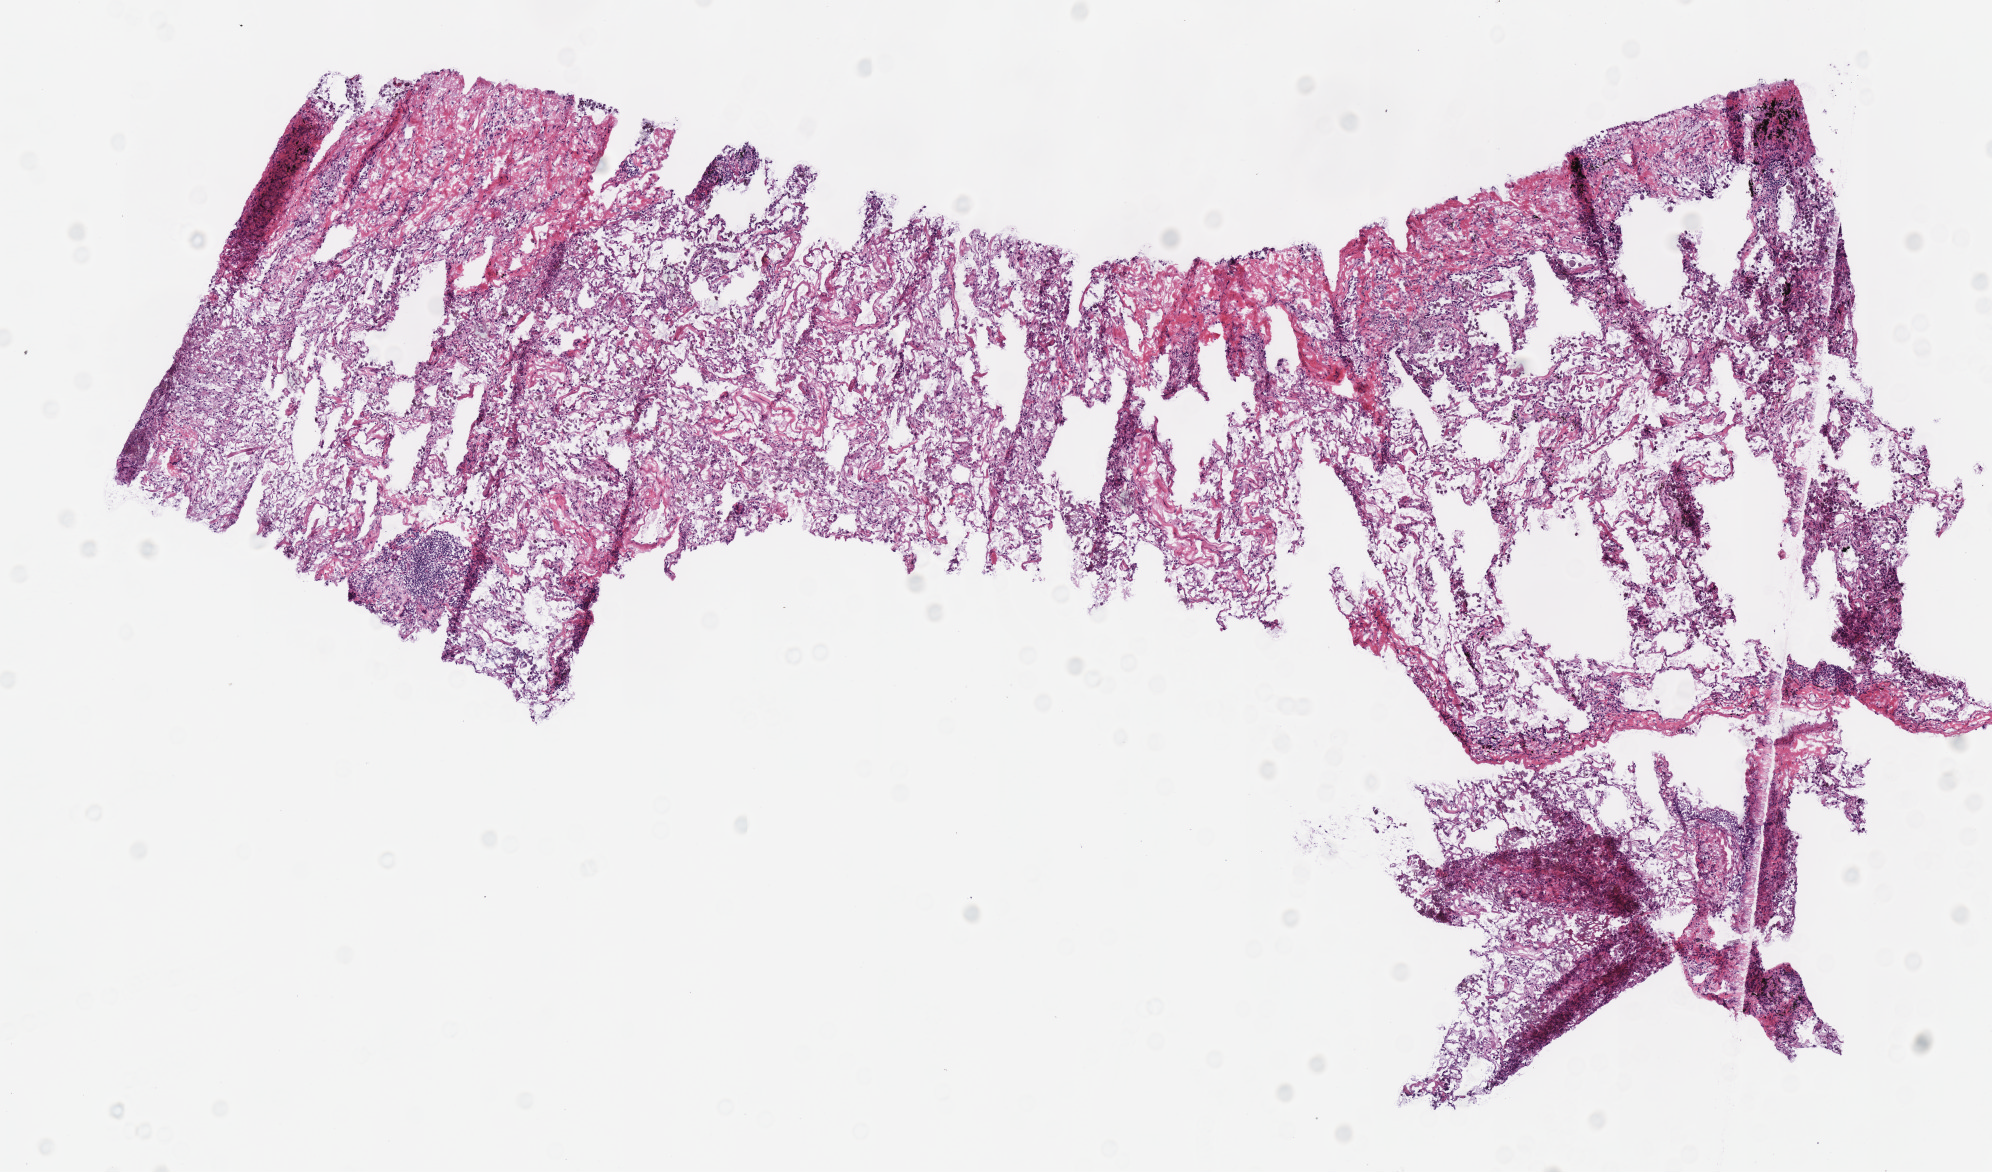
Digitized H&E tissue section (whole slide) — low-resolution overview of the scanned area, about 7.8 x 4.6 mm, frozen section from the top of the tissue portion, sample: solid tissue normal (non-tumour tissue), lung. Male, age 70 years at initial diagnosis.
This section: solid tissue normal sample (biorepository sample class). Patient diagnosis: Adenocarcinoma, NOS (upper lobe, lung).